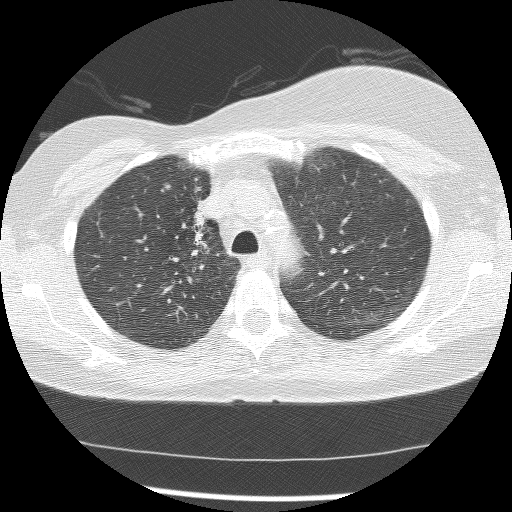
Chest CT (low-dose screening protocol), one axial image, first (baseline) screen, lung window (W 1500 / L -600 HU), 2.5 mm slice thickness, lung (sharp) reconstruction kernel (BONE), slice 40 of 172 in the series. Female participant, aged 56 years at enrolment. Current smoker at enrolment.
Lesion marked by an expert reader, bounding box <165,191,223,272> (left, top, right, bottom; pixels). The screening reader recorded 2 non-calcified nodules or masses ≥4 mm on this exam; which of them this box marks is not recorded. Official screen result: positive, change unspecified: nodule(s) >= 4 mm or enlarging nodule(s), mass(es), or other non-specific abnormalities suspicious for lung cancer. Participant outcome: lung cancer diagnosed 1185 days after this screen (after the third annual screen) — adenocarcinoma, NOS, right upper lobe, stage IIIB (AJCC 6th edition), 8 mm at pathology.